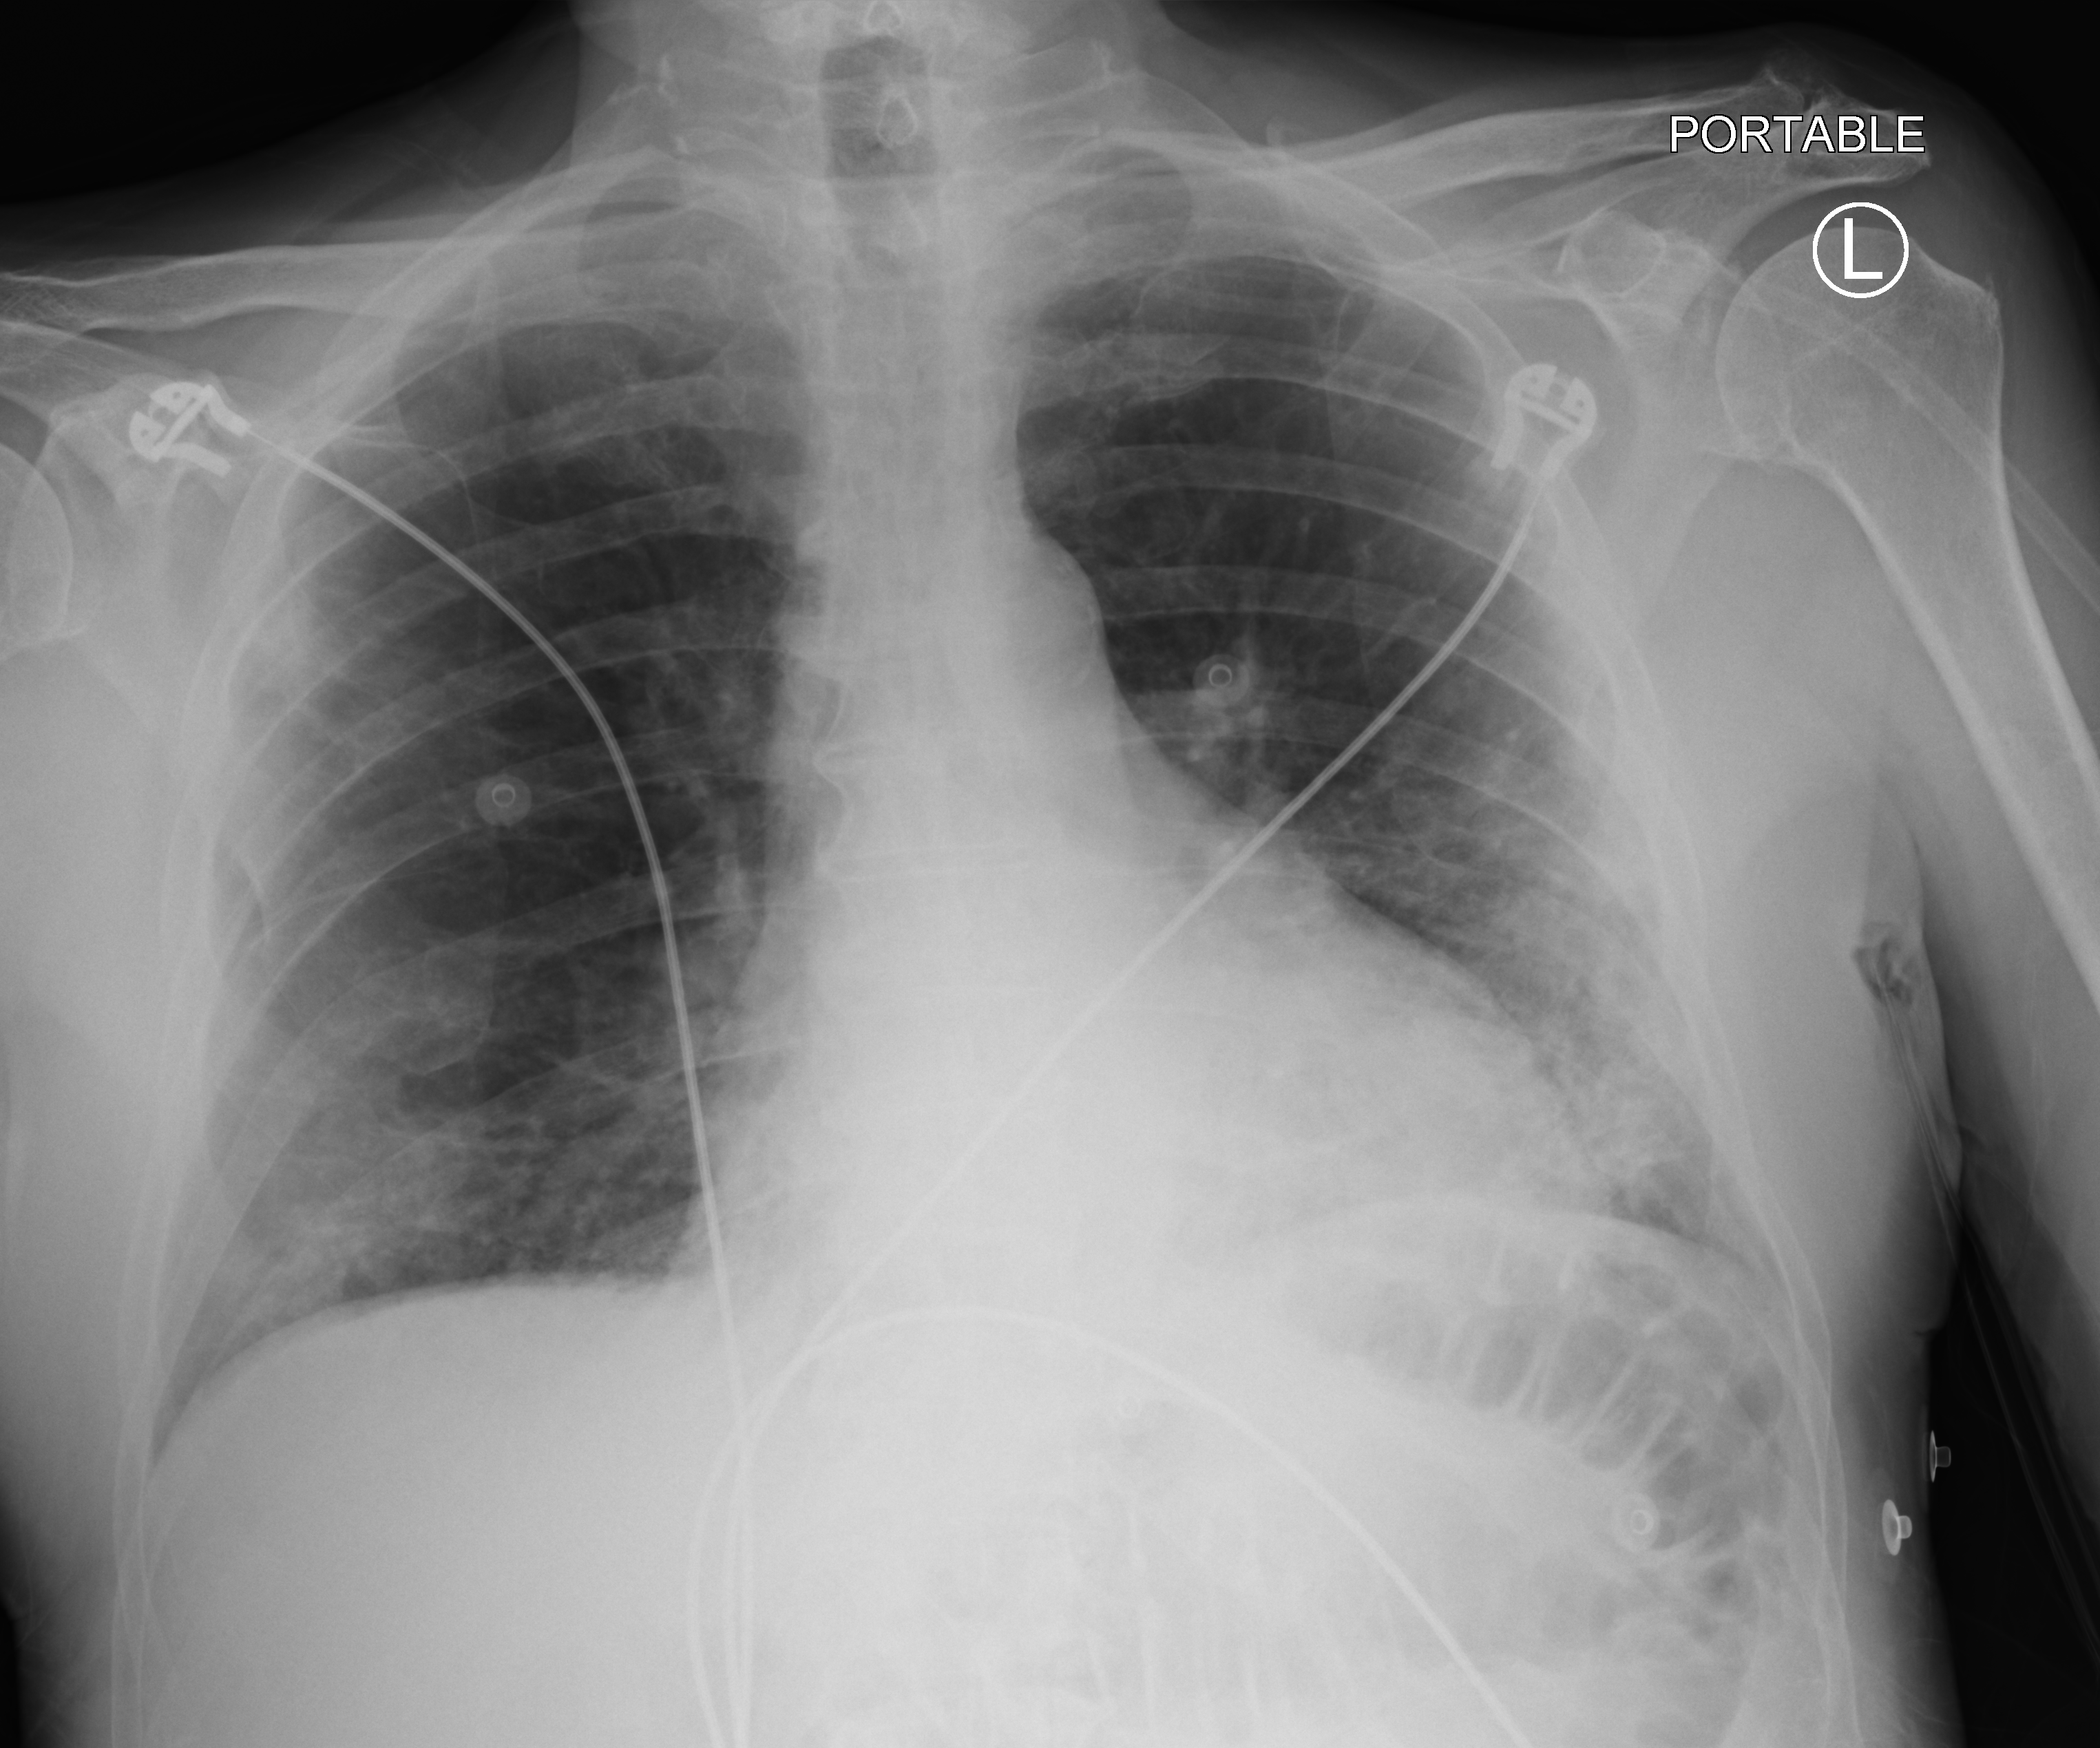
Bedside chest radiograph (computed radiography), anteroposterior (AP) projection. Male patient hospitalised with COVID-19, age 75–90 years.
Admission-level facts for this patient (not findings on this image; timing relative to this image not recorded): admitted to intensive care during this hospital stay: no.